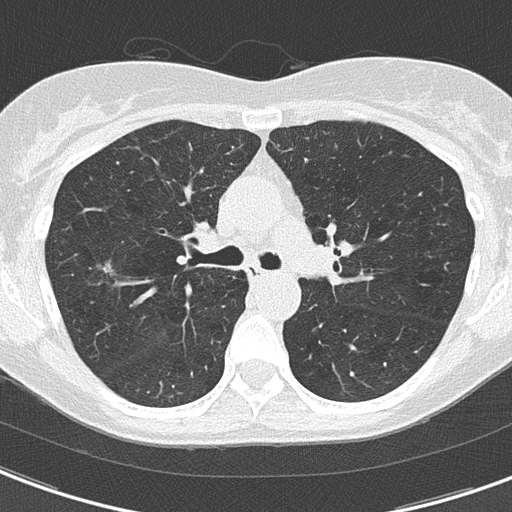
Axial slice from a low-dose chest CT screening exam, second annual screen, lung window (W 1500 / L -600 HU), lung (sharp) reconstruction kernel (B50f), 120 kVp, slice 56 of 156 in the series, 512 × 512 image matrix, field of view 280 × 280 mm. Female participant, aged 59 years at enrolment.
• Expert-annotated lung lesion, bounding box (x1, y1, x2, y2) in pixels: (84, 250, 137, 290).
• Screening reader's record for this exam (one nodule recorded; not confirmed to be the boxed lesion): non-calcified nodule or mass ≥4 mm, right upper lobe, 7 × 6 mm, poorly defined margins, ground glass attenuation, pre-existing on the prior screen: yes; interval growth: no.